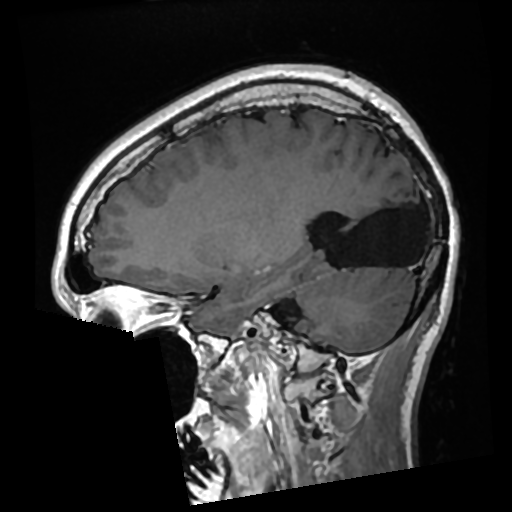
Brain MRI from a brain-tumour surgery series, one sagittal slice; slice 104 of 276 in the series (ordered by position); T1-weighted post-contrast; 0.7 mm slice thickness; 512 × 512 image matrix, field of view 250 × 250 mm. Case-level facts recorded for this patient, not image findings: histopathology: Glioma with ependymal features; WHO grade: 2; tumour location: Left Parietal.
Annotated regions visible in this slice (expert manual segmentation):
- previous resection cavity: bounding box (x1, y1, x2, y2) in pixels: (327, 184, 424, 268)